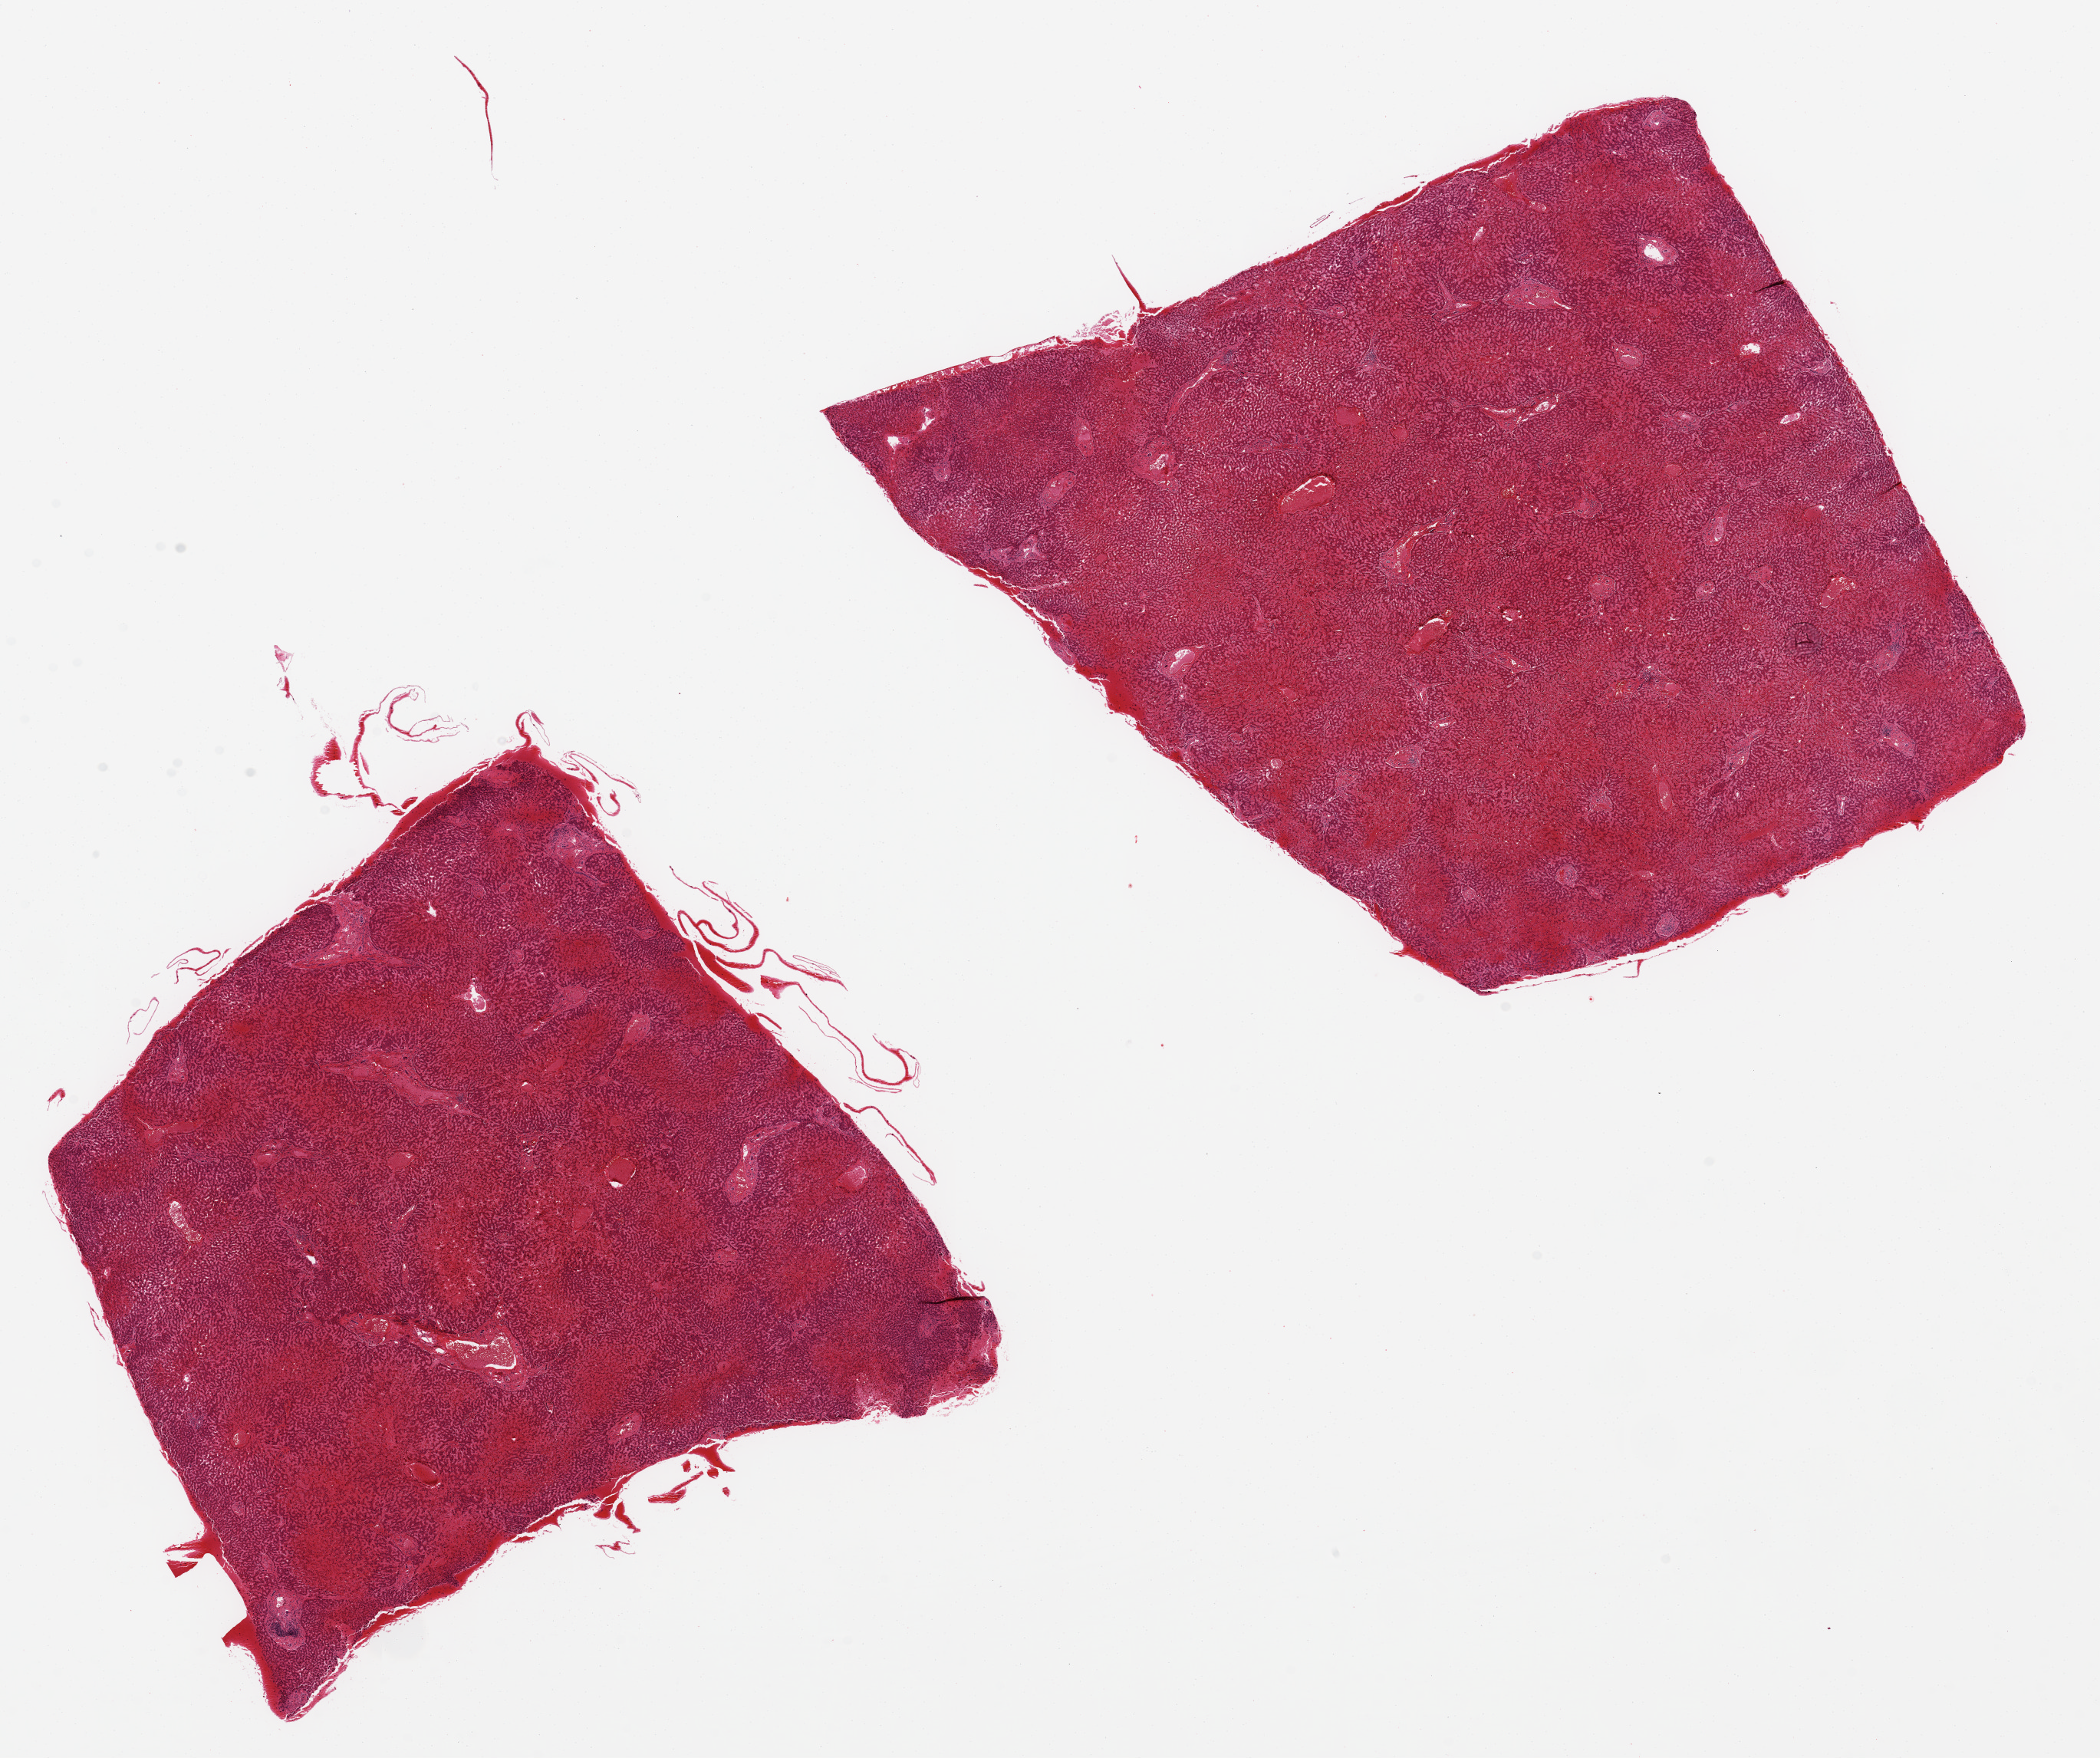
H&E whole-slide image, whole scanned area (about 21.7 x 18.1 mm) shown as a low-resolution overview. PAXgene-fixed paraffin-embedded (PFPE) section. Sampled site (target tissue): liver. Donor tissue sample. Donor sex: male.
Reviewer comment on this tissue sample: 2 pieces, 9x8 & 8x8 mm; severe central passive congestion.